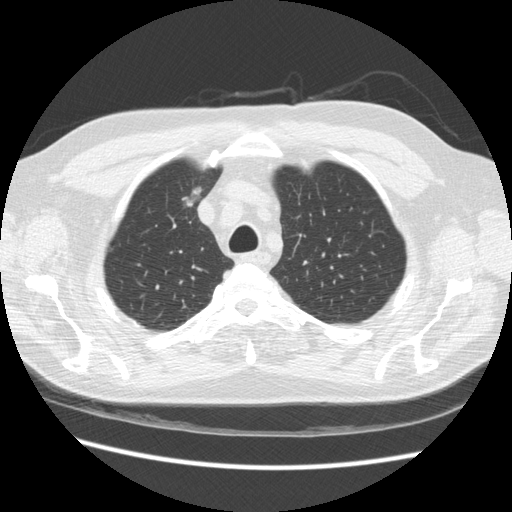
Chest CT (low-dose screening protocol), one axial image, third annual screen, lung window (W 1500 / L -600 HU), slice 50 of 234 in the series, 512 × 512 image matrix. Male, age 66 years at enrolment. Former smoker at enrolment.
Expert reader's lesion annotation, bounding box [x1, y1, x2, y2] px = [165, 176, 213, 219]. Screening reader's record for this exam: no non-calcified nodule ≥4 mm recorded. Lung cancer was diagnosed 229 days after this screen: bronchiolo-alveolar adenocarcinoma, NOS, right upper lobe, moderately differentiated (G2), stage IA (AJCC 6th edition), 12 mm at pathology.